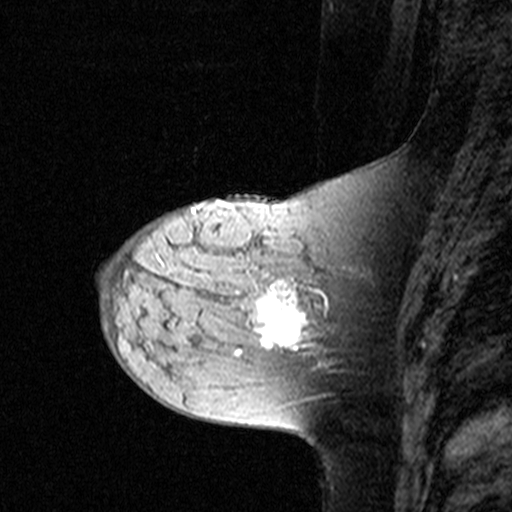
Breast MRI (dynamic contrast-enhanced), one sagittal slice; slice 13 of 44 in the series (ordered by position); dynamic contrast-enhanced study with each time point stored as its own series, time point 2 of 3 at this slice position (early post-contrast, ordered by acquisition time); 1.5 T; TE 4.5 ms, TR 11 ms; 3 mm slice thickness; 512 × 512 image matrix. Female patient, age 44 years. From the clinical record (not read from this slice): setting: breast cancer imaged before/during neoadjuvant chemotherapy; receptor status: triple-negative.
Outlined on this slice (semi-automatic segmentation, software-assisted and operator-edited):
- analysis volume of interest (the breast-tissue region the enhancement analysis was run in; not a lesion): bounding box <142,208,349,363> (left, top, right, bottom; pixels)
- tumour enhancement mask (voxels above the 90 % enhancement threshold inside the analysis volume of interest): <262,280,327,350>